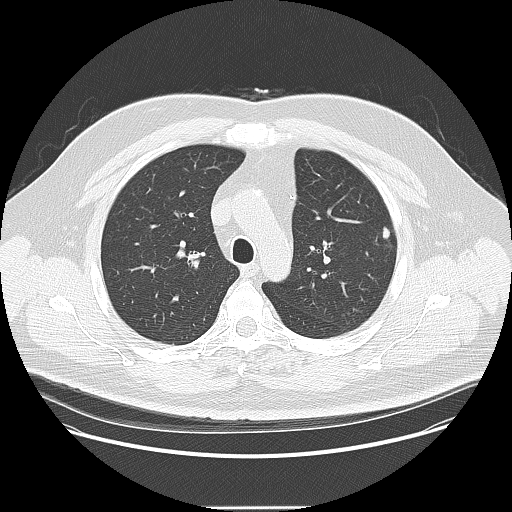
Low-dose screening chest CT, one axial slice. Slice 110 of 157 in the series (ordered by position). Reconstruction kernel LUNG. 120 kVp. Lung window (W 1500 / L -600 HU). 2.5 mm slice thickness. 512 × 512 image matrix.
Structures marked on this image (expert manual segmentation):
- lesion 1 (tumor, upper lobe of left lung): box from (x=382, y=227) to (x=390, y=239) px